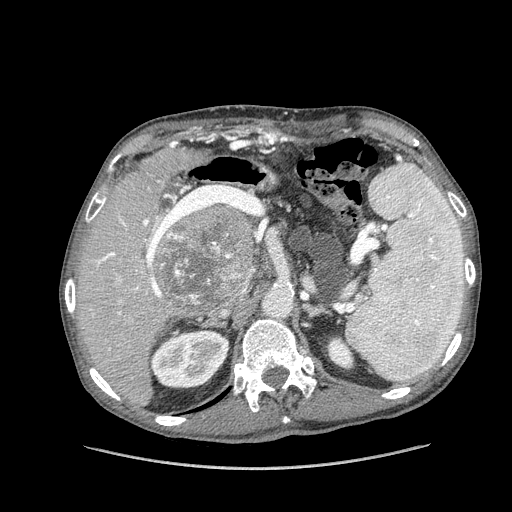
Contrast-enhanced abdominal CT (liver protocol), one axial slice; slice 83 of 162 in the series (ordered by position); 100 kVp; soft-tissue window (W 400 / L 40 HU); 2.5 mm slice thickness; 512 × 512 image matrix, field of view 400 × 400 mm. Case-level facts recorded for this patient, not image findings: diagnosis: hepatocellular carcinoma (patient treated with transarterial chemoembolisation; whether this scan precedes or follows treatment is not stated here); TNM stage (as recorded): Stage-IIIA; Child-Pugh class: A; tumour nodularity: multinodular; tumour size: 9.9 cm.
Annotated regions visible in this slice (semi-automatically segmented with operator editing):
- liver parenchyma outside the tumour (the mass and vessels are separate outlines, so this box may not span the whole liver): bounding box <76,144,254,406> (left, top, right, bottom; pixels)
- mass: <154,202,258,308>
- liver vessels: <96,144,180,350>